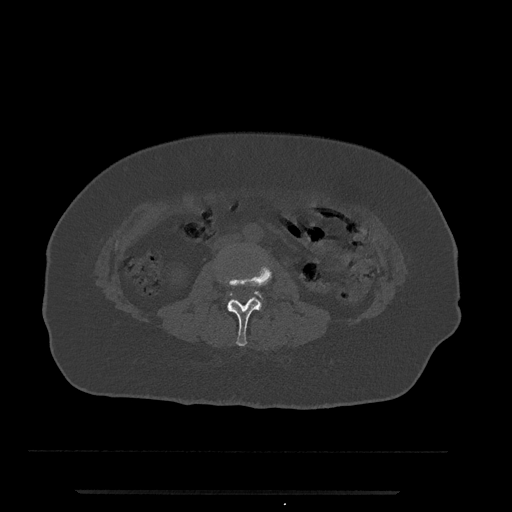
CT including the spine, one axial slice. Position 12 of 797 along the scan axis. 120 kVp. Bone window (W 1800 / L 400 HU). 0.5 mm slice thickness. 512 × 512 image matrix. Female patient, age 51 years. From the clinical record (not read from this slice): primary cancer: neuro; vertebrae with lytic lesions (as recorded): T8.
Structures marked on this image (semi-automatic segmentation, software-assisted and operator-edited):
- L2 vertebra: bounding box <218,257,273,346> (left, top, right, bottom; pixels)